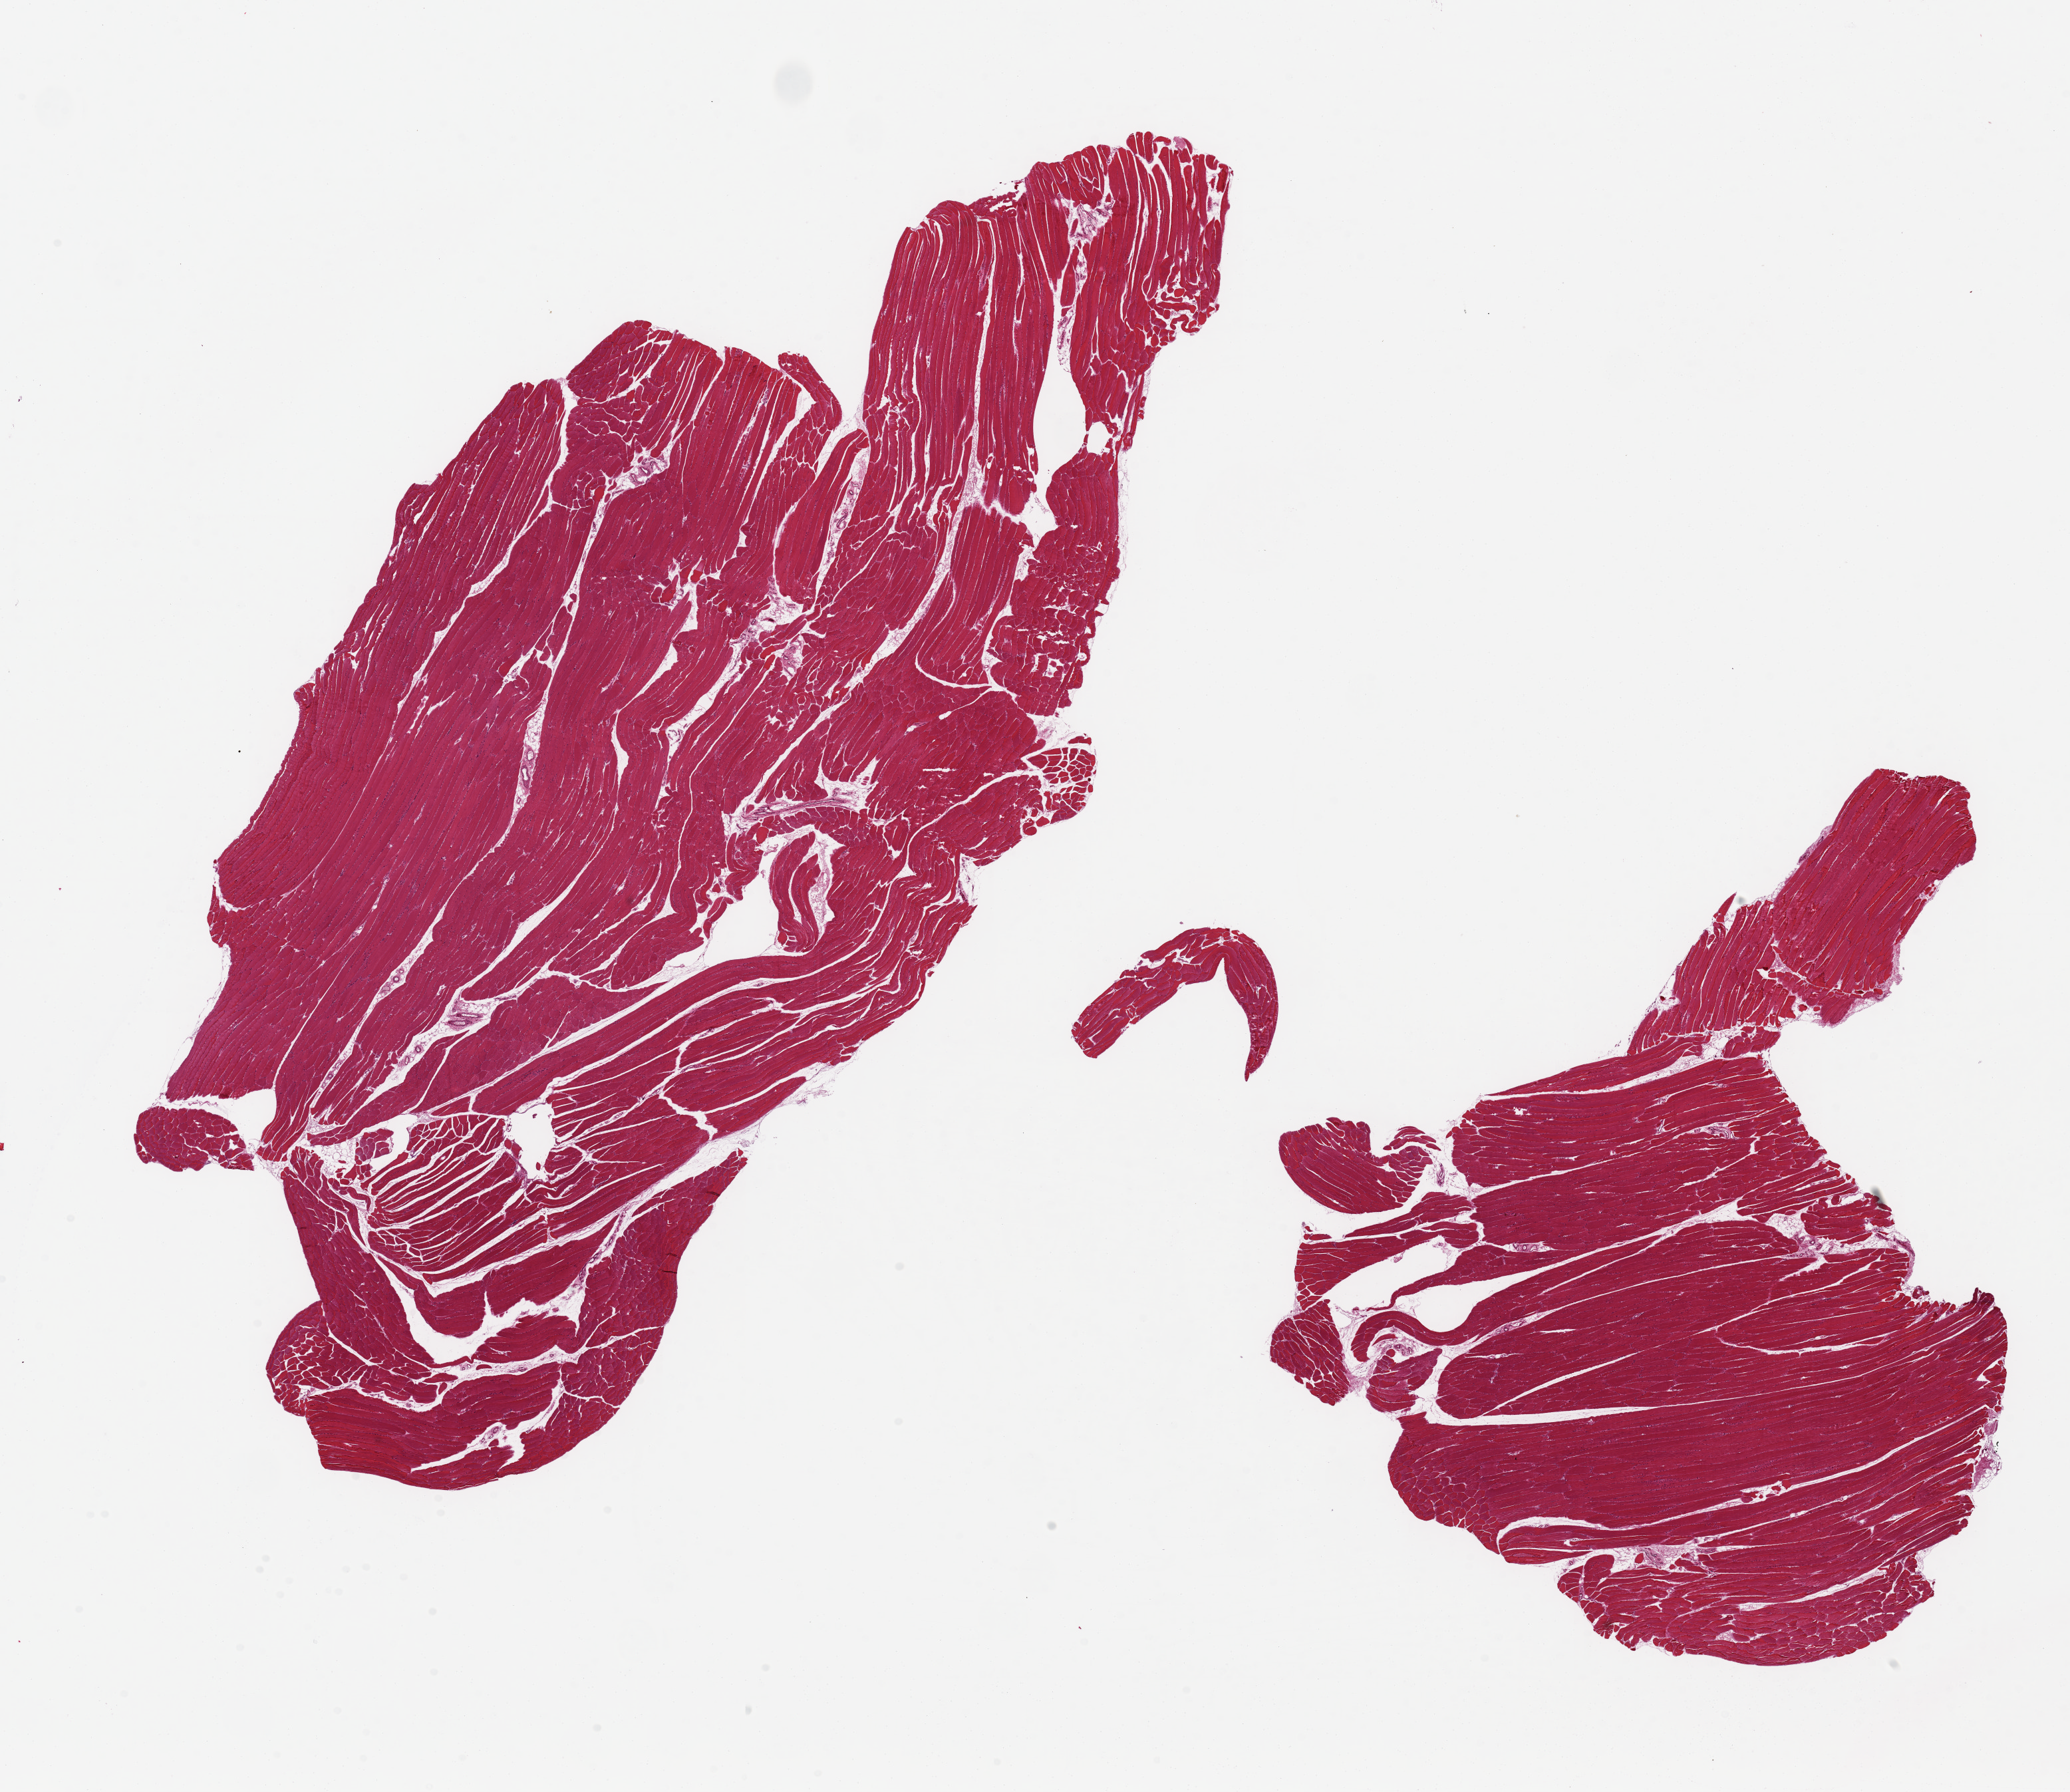
Digitized hematoxylin and eosin (H&E)-stained section — a low-resolution overview of the entire scanned area, about 24.6 x 21.3 mm. PAXgene-fixed, paraffin-embedded tissue. Section of skeletal muscle (target tissue). Donor tissue sample. Donor: male.
Reviewer comment on this tissue sample: 2 pieces, 18.3x6.8 & 8.5x8.4 mm; no extraneous adipose.